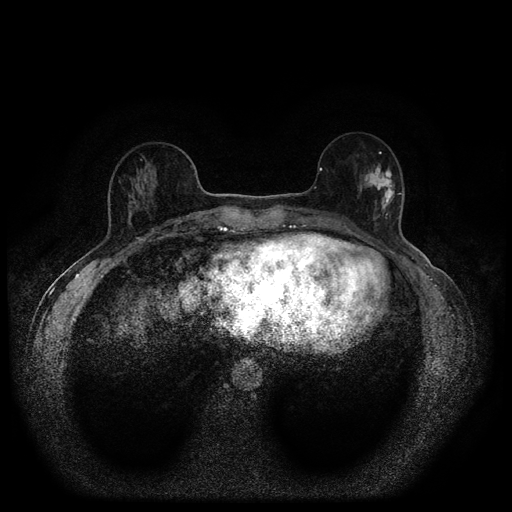
Breast MRI (dynamic contrast-enhanced, multi-phase), one axial slice; position 37 of 116 along the scan axis; dynamic contrast-enhanced series, time point 2 of 5 at this slice position (early post-contrast); 1.5 T; TE 2.7 ms, TR 5.4 ms; 512 × 512 image matrix, field of view 330 × 330 mm. Female patient, age 56 years.
Structures marked on this image (semi-automatic segmentation, software-assisted and operator-edited):
- breast lesion (labelled 'tumour' in the annotation; benign lesions carry a separate 'benign' label): bounding box <359,159,398,219> (left, top, right, bottom; pixels)